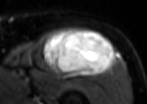
MRI of an extremity soft-tissue mass, one axial slice; slice 64 of 85 in the series (ordered by position); T2-weighted fat-saturated; MR volume resampled by the dataset authors to the PET/CT grid (not the native acquisition matrix); 147 × 104 image matrix. Male patient. Case-level facts recorded for this patient, not image findings: histological type: extraskeletal osteosarcoma; grade: high; site of the primary tumour: thigh.
Structures marked on this image (expert contour drawn on MRI and transferred to this co-registered scan by the dataset authors):
- gross tumour volume (mass): bounding box <42,28,114,75> (left, top, right, bottom; pixels)